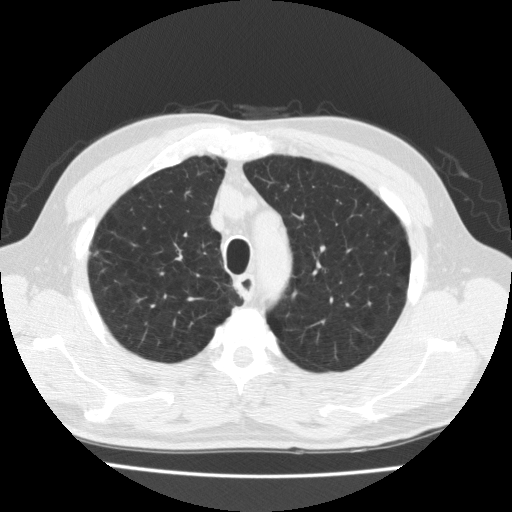
Low-dose screening chest CT, one axial slice. Slice 170 of 205 in the series (ordered by position). Reconstruction kernel FC10. 120 kVp. Lung window (W 1500 / L -600 HU). 2 mm slice thickness. 512 × 512 image matrix.
Annotated regions visible in this slice (outlined manually by an expert reader):
- lesion 1 (tumor, upper lobe of right lung): bounding box [x1, y1, x2, y2] px = [93, 251, 99, 256]